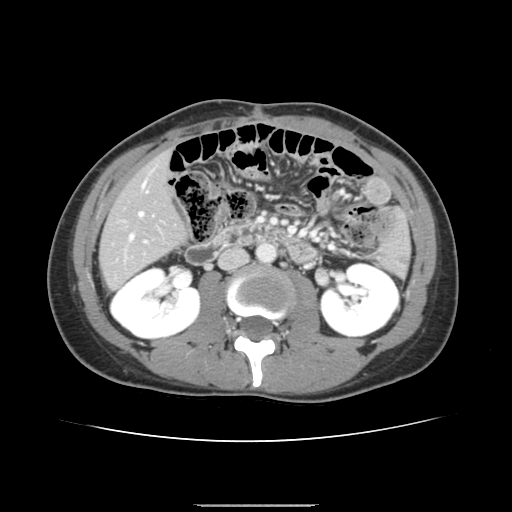
Contrast-enhanced abdominal CT, one axial slice. Position 57 of 150 along the scan axis. 120 kVp. Intravenous contrast given. Soft-tissue window (W 400 / L 40 HU). 2.5 mm slice thickness. 512 × 512 image matrix, field of view 324 × 324 mm. Female patient, age 32 years. From the clinical record (not read from this slice): diagnosis: colorectal cancer liver metastases, imaged before liver resection; multiple liver metastases: yes; largest metastasis: 0.7 cm; chemotherapy before resection: yes.
Annotated regions visible in this slice (expert manual segmentation):
- hepatic veins: bounding box [x1, y1, x2, y2] px = [130, 181, 146, 239]
- liver: [100, 154, 186, 288]
- planned liver remnant (the part of the liver to remain after resection): [100, 154, 186, 288]
- portal vein (with intrahepatic branches): [144, 240, 147, 242]